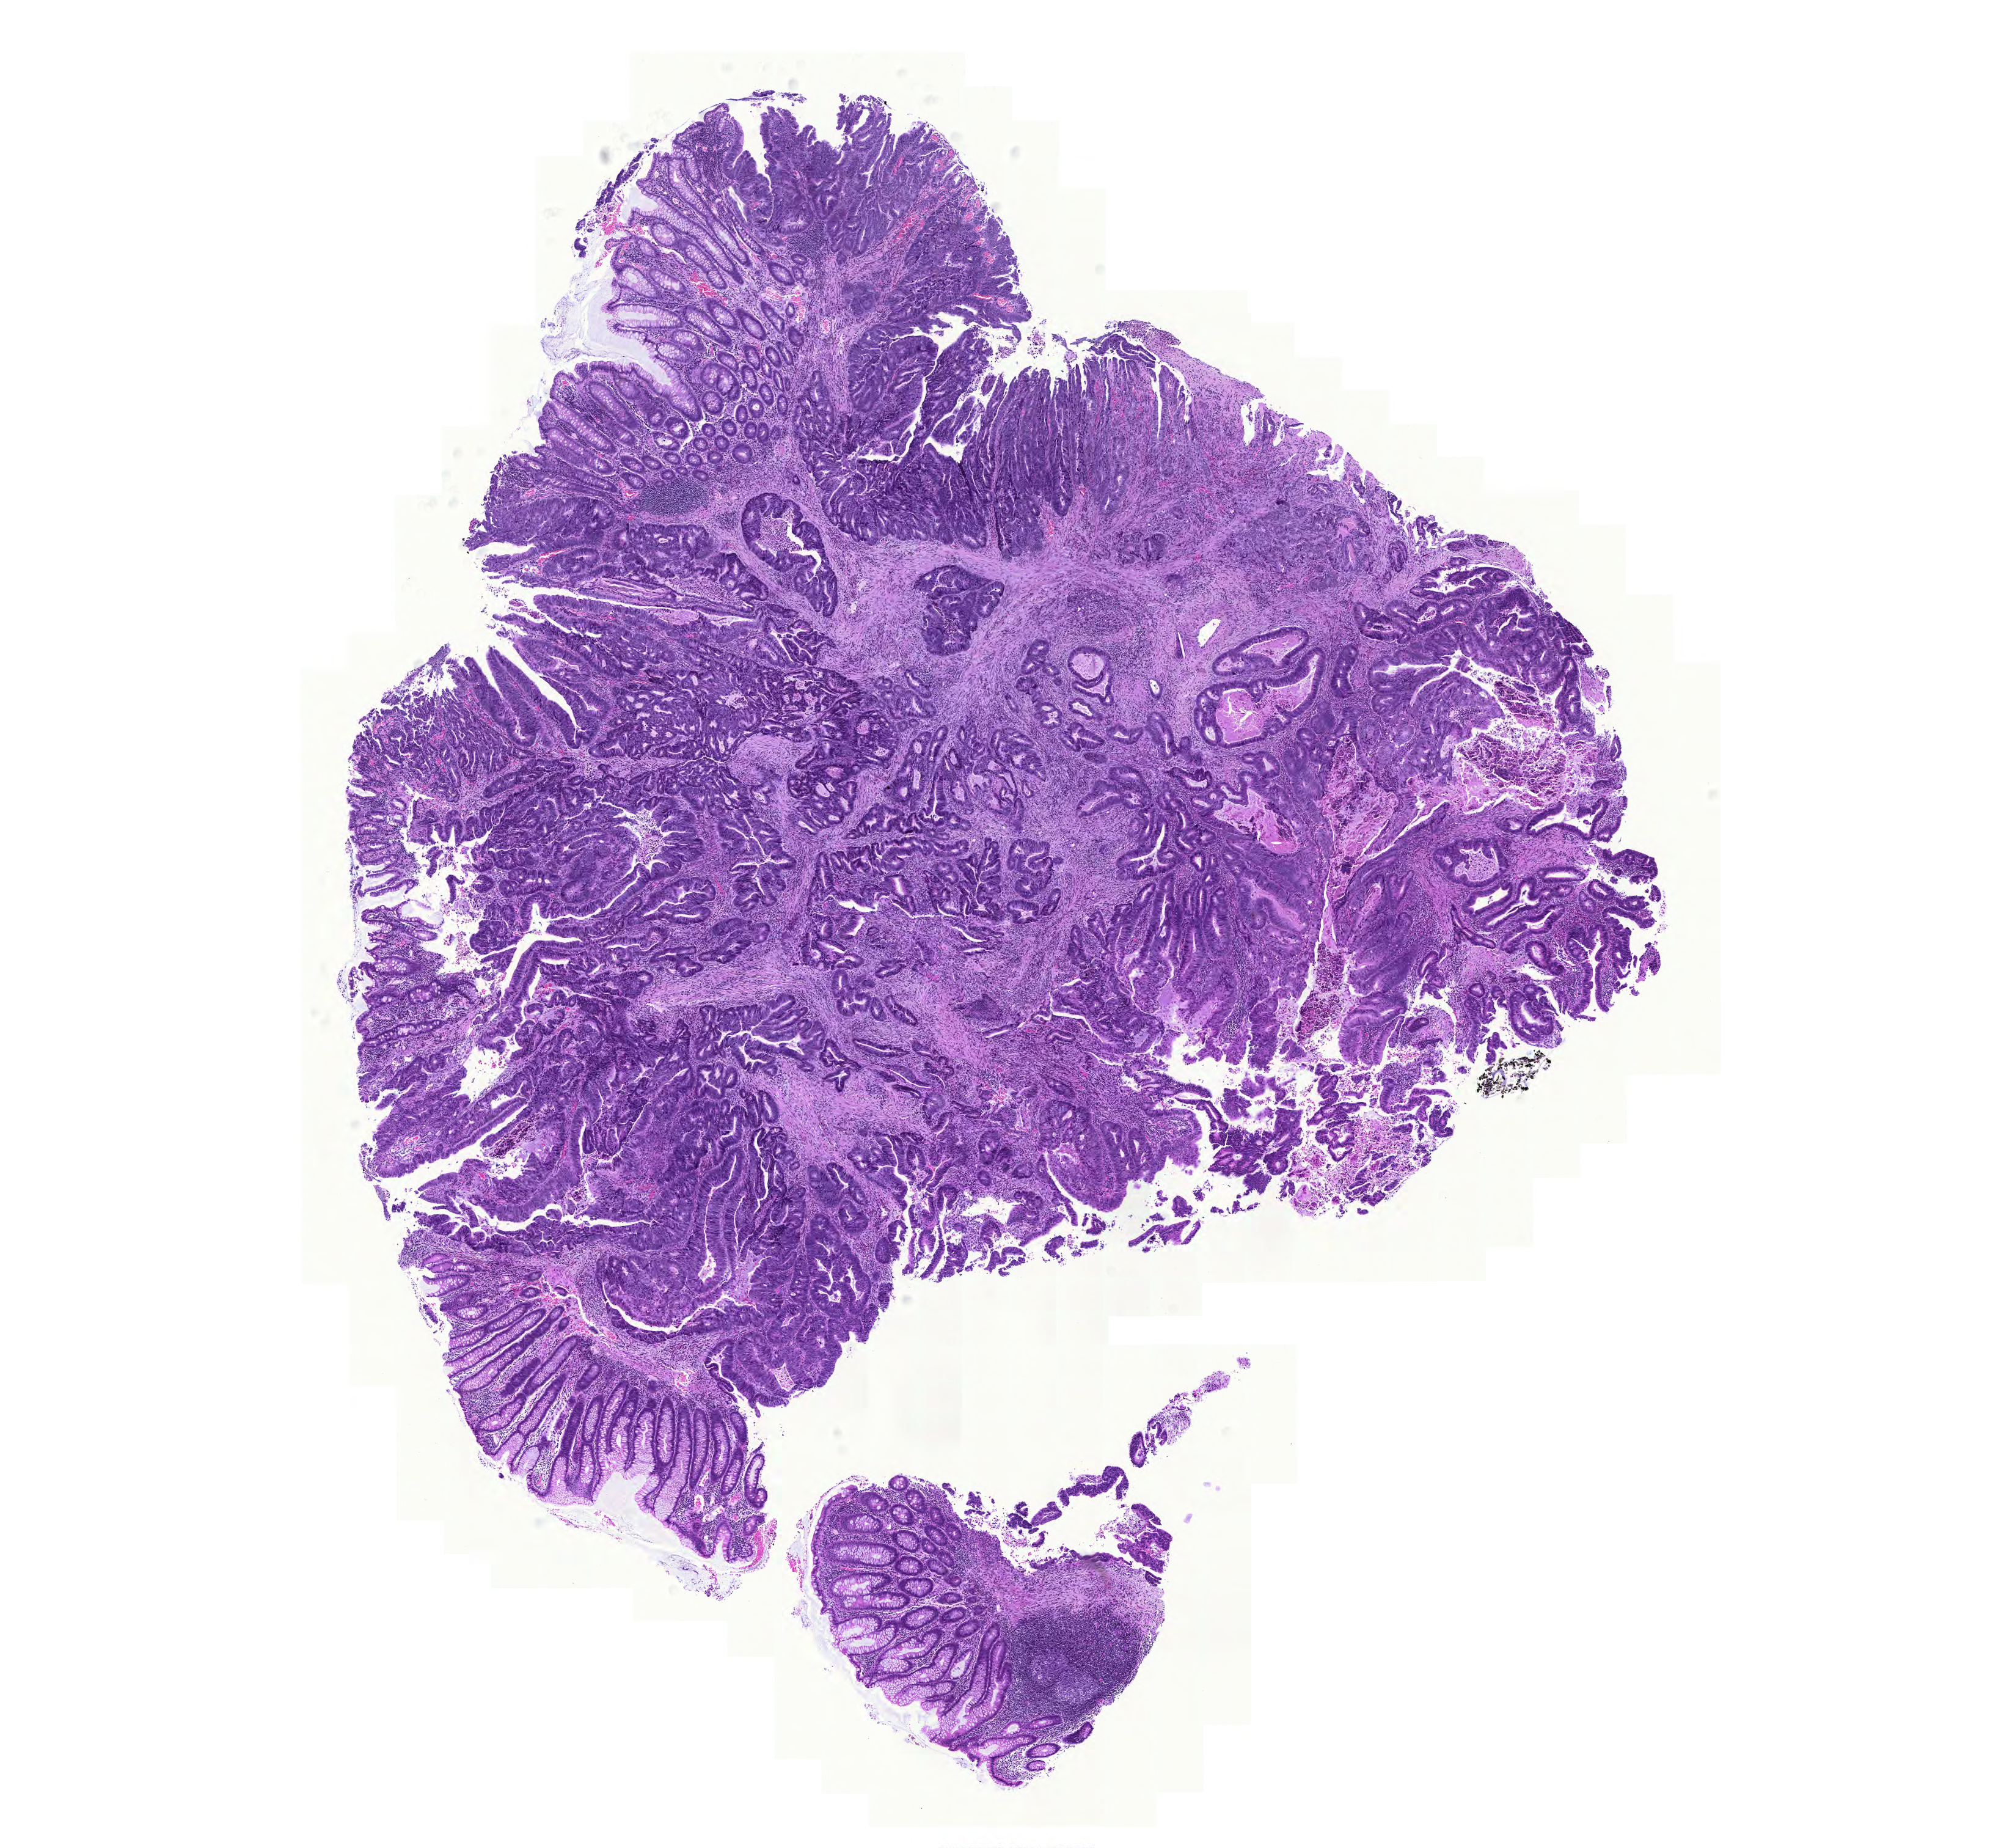
Hematoxylin and eosin (H&E) stained whole-slide image, whole scanned area (about 12.2 x 11.2 mm) shown as a low-resolution overview, FFPE section, primary tumour sample from the colon. Male, age 65 years at initial diagnosis.
Pathologic diagnosis: Adenocarcinoma, NOS (cecum).